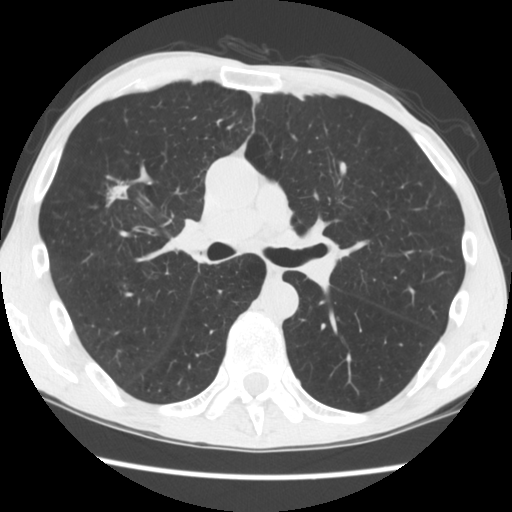
Chest CT (low-dose screening protocol), one axial image, second screening round (one year after baseline), lung window (W 1500 / L -600 HU), 2.5 mm slice thickness, standard (soft-tissue) reconstruction kernel (STANDARD), slice 78 of 181 in the series. Male, age 56 years at enrolment. Current smoker at enrolment.
Expert-annotated lung lesion, bounding box (x1, y1, x2, y2) in pixels: (93, 174, 147, 230). The screening reader recorded 2 non-calcified nodules or masses ≥4 mm on this exam; which of them this box marks is not recorded. Participant outcome: lung cancer diagnosed 101 days after this screen — squamous cell carcinoma, NOS, right upper lobe, right middle lobe, well differentiated (G1), stage IA (AJCC 6th edition), 27 mm at pathology.